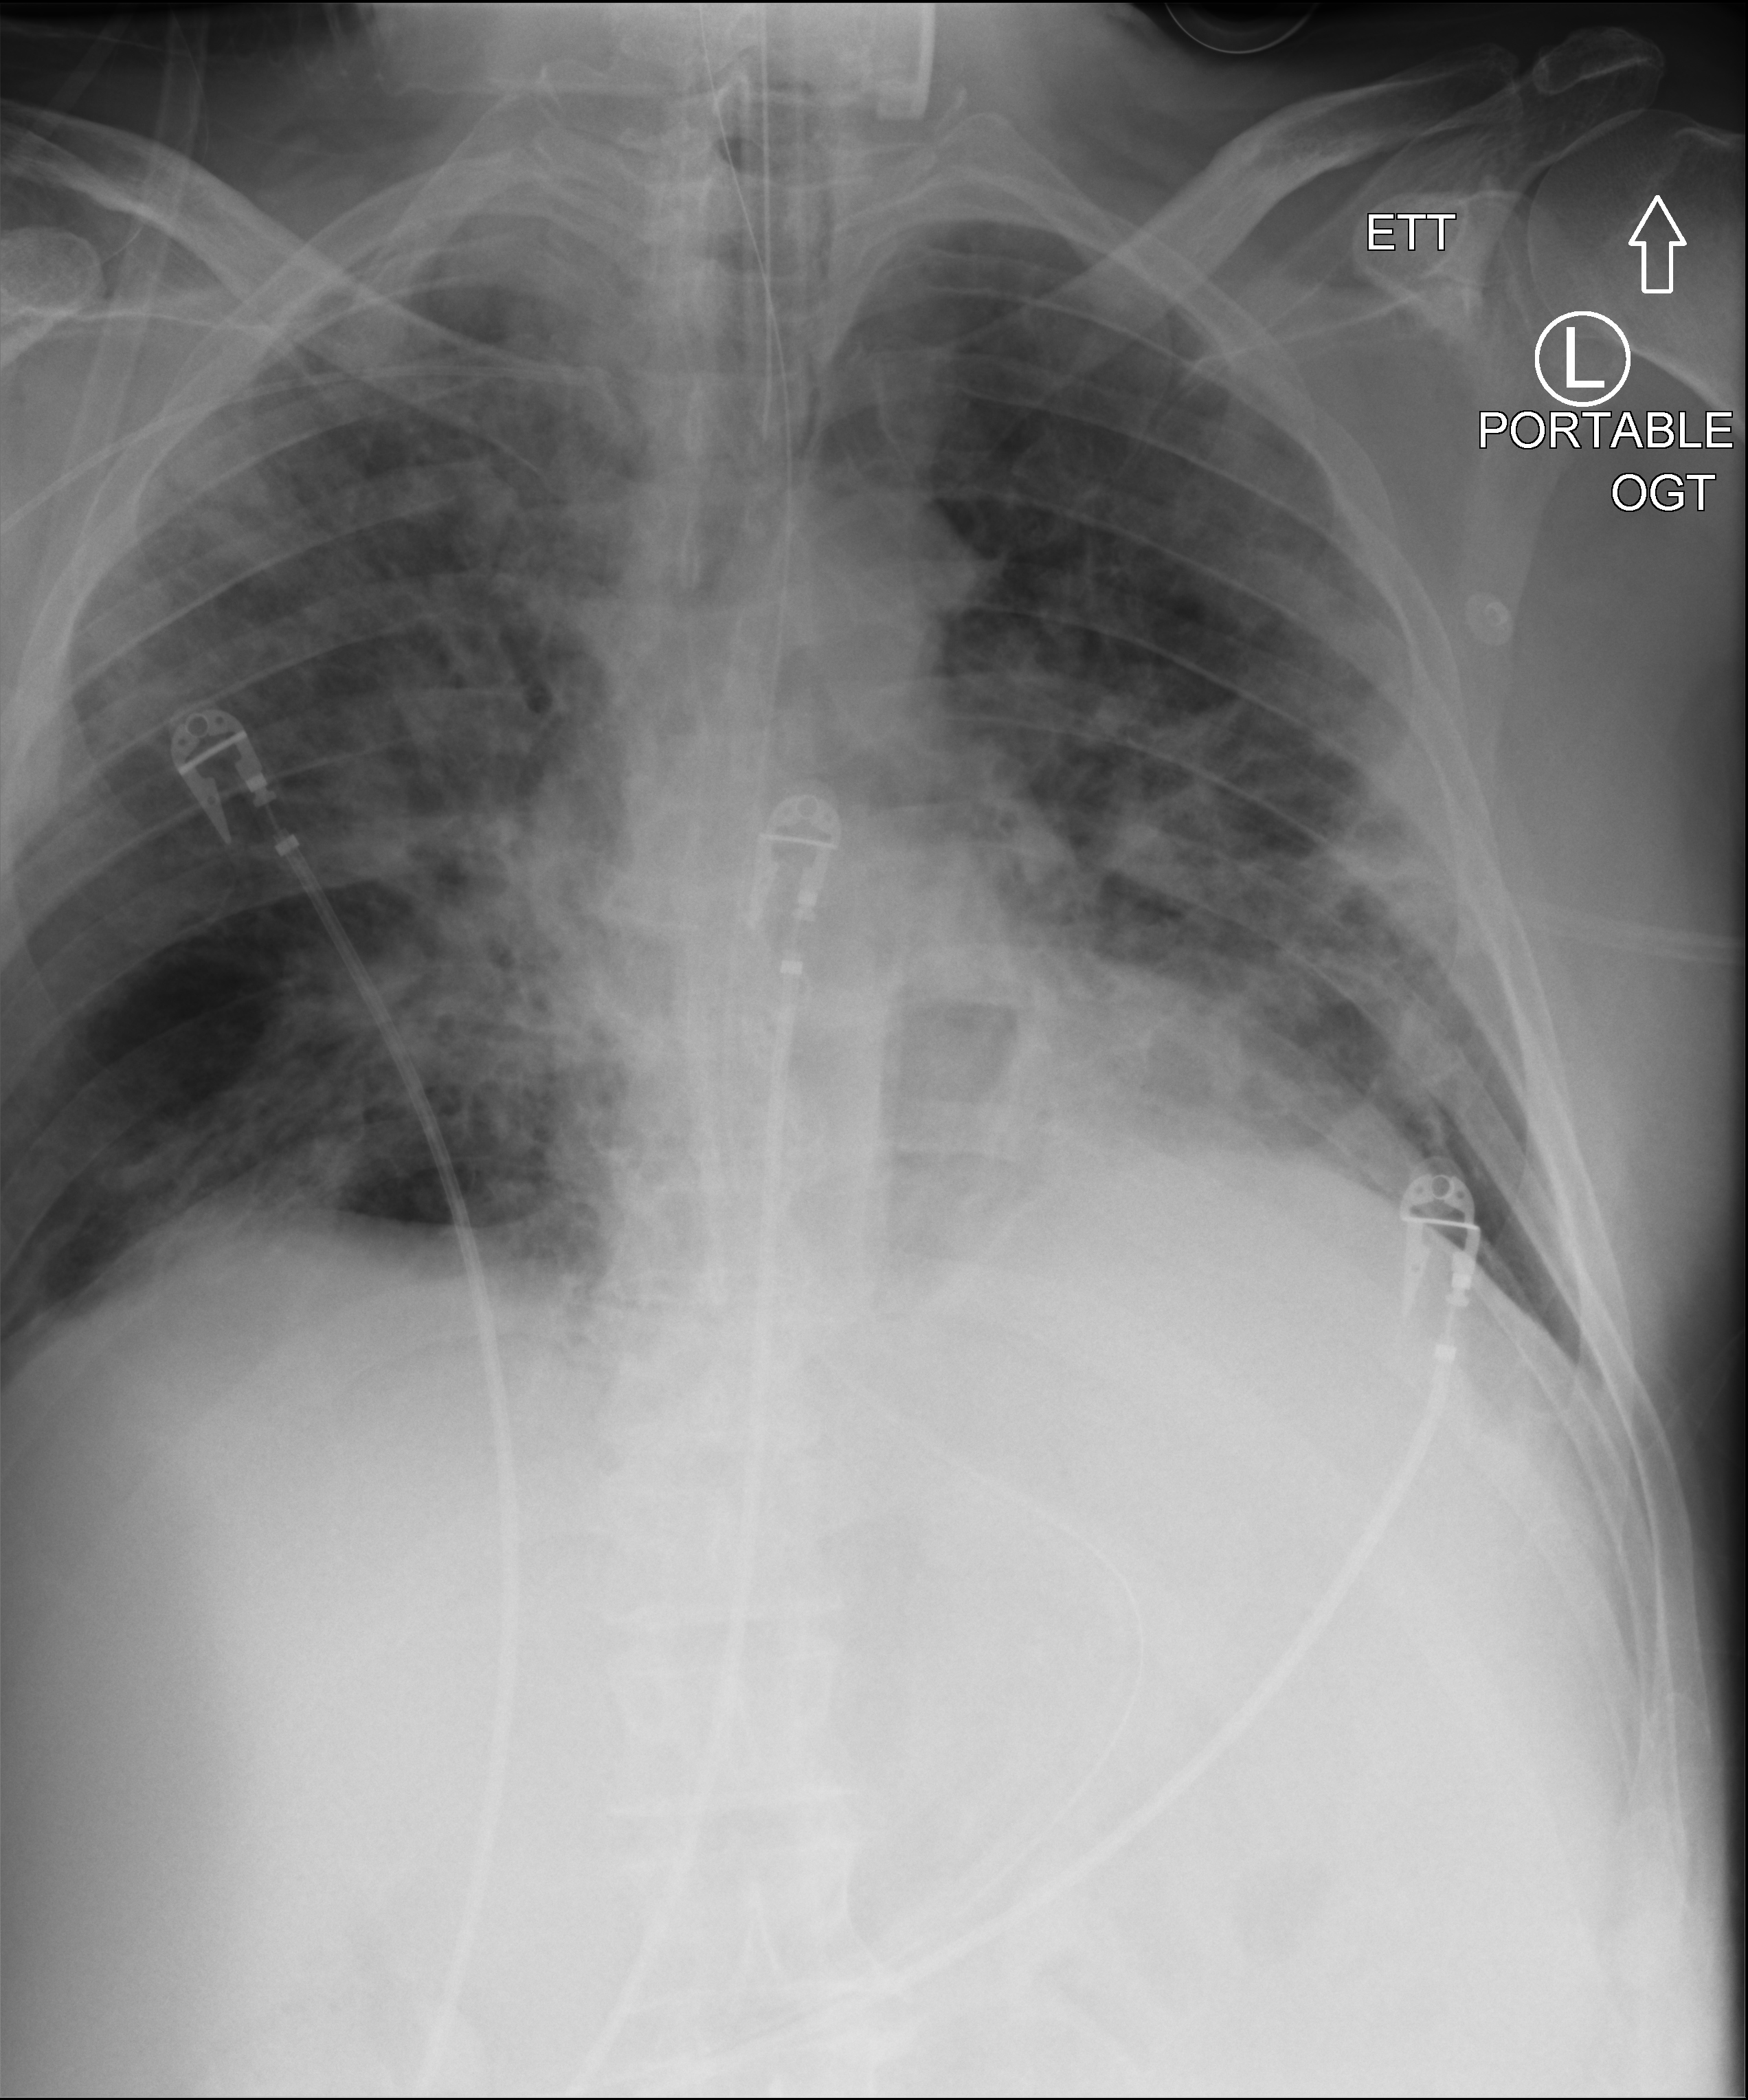
Portable chest radiograph, anteroposterior (AP) projection. Patient hospitalised with COVID-19; male, aged 60–74 years.
Hospital-stay facts (about this admission, not read from this image; timing relative to this image not recorded):
- mechanically ventilated during this hospital stay: yes